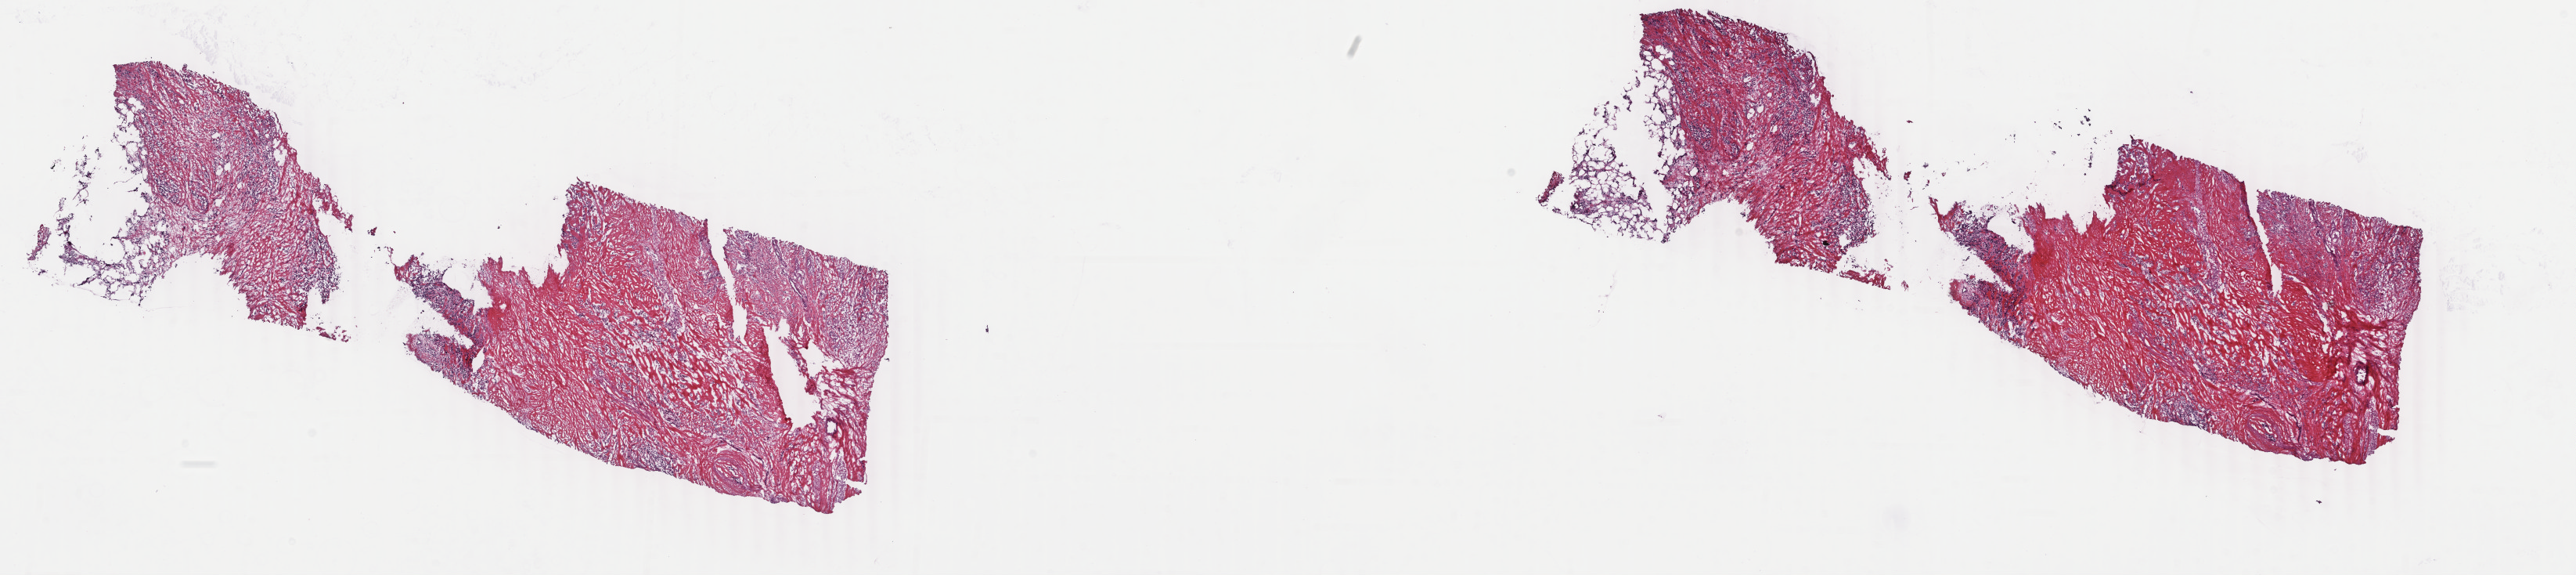
H&E-stained whole-slide image — low-resolution overview of the scanned area, about 26.2 x 5.8 mm (acquisition: 40x scan). Frozen section from the top of the tissue portion. Breast, primary tumour sample. Female patient; age at initial diagnosis 64 years. Pathologist review of this section (percent, as recorded): tumour cells 65%, tumour nuclei 80%, normal cells 0%, stromal cells 35%, necrosis 0%. Infiltration values recorded for this section: lymphocyte infiltration 0%, monocyte infiltration 0%, neutrophil infiltration 0%.
Laterality: right. AJCC pathologic stage: IIA (6th edition). Histologic diagnosis: Lobular carcinoma, NOS.